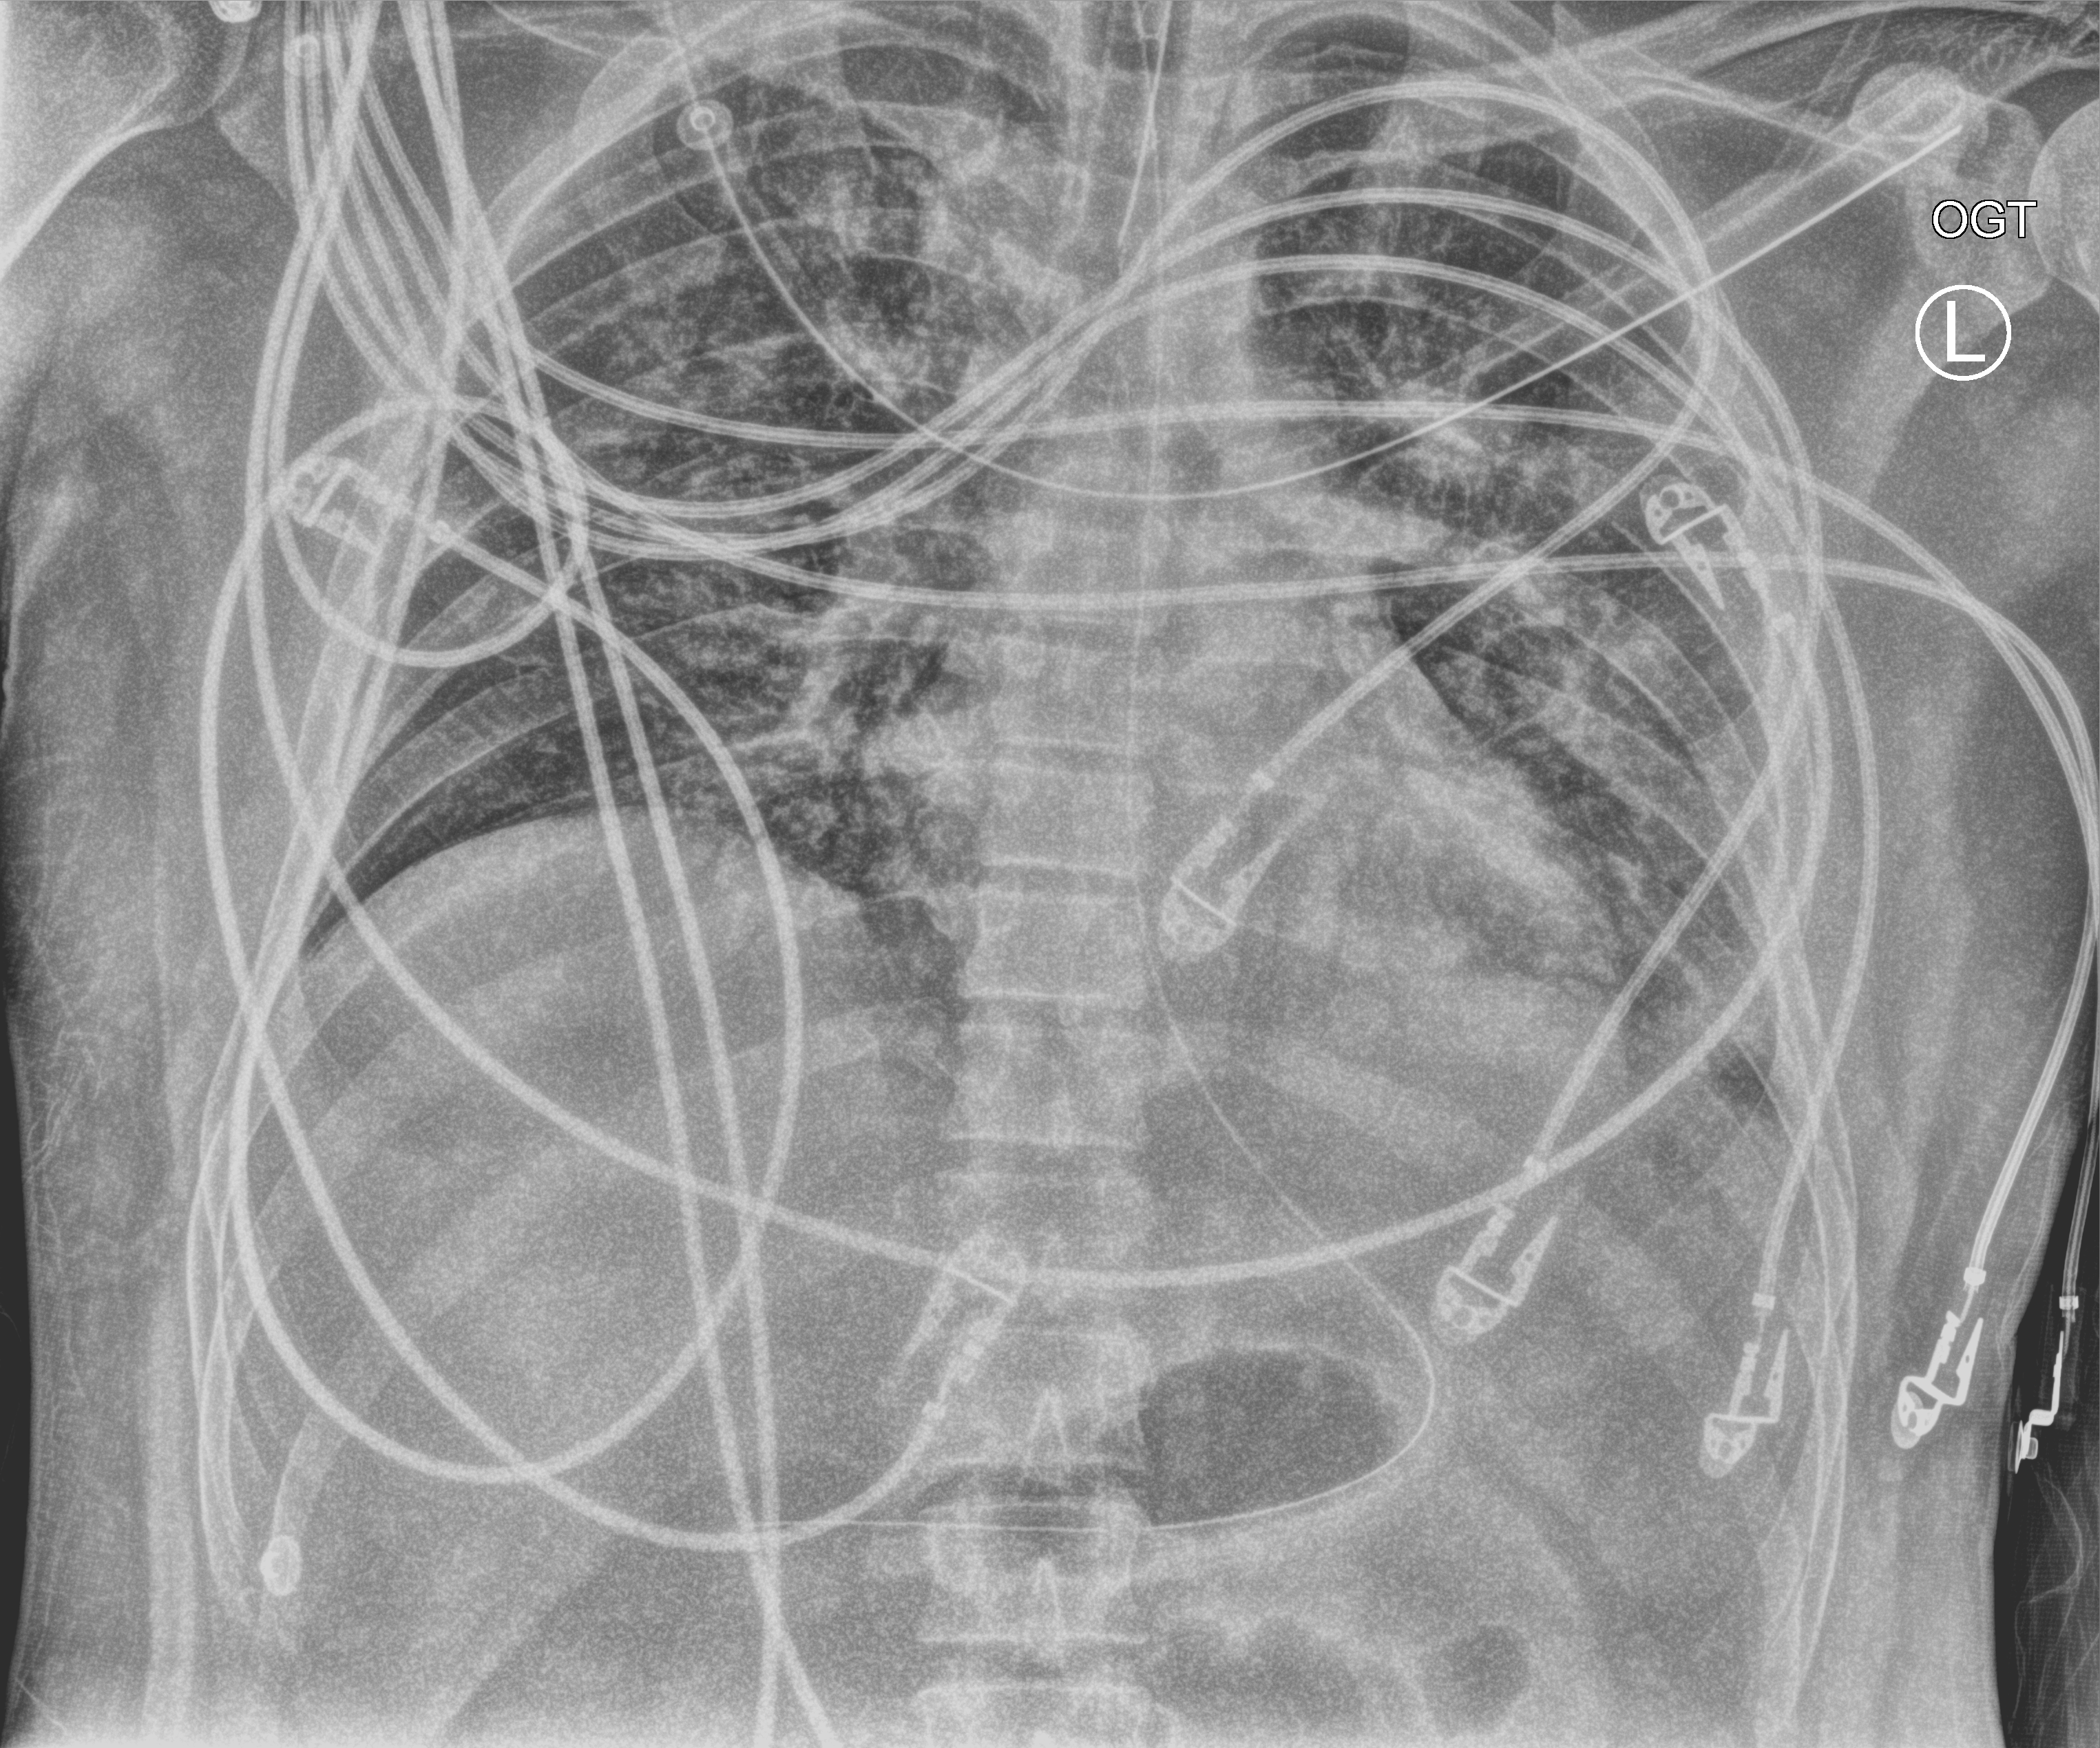
Portable chest radiograph, anteroposterior (AP) projection. Patient hospitalised with COVID-19, aged 18–59 years.
Hospital-stay facts (about this admission, not read from this image; timing relative to this image not recorded):
- chronic kidney disease (admission record): no